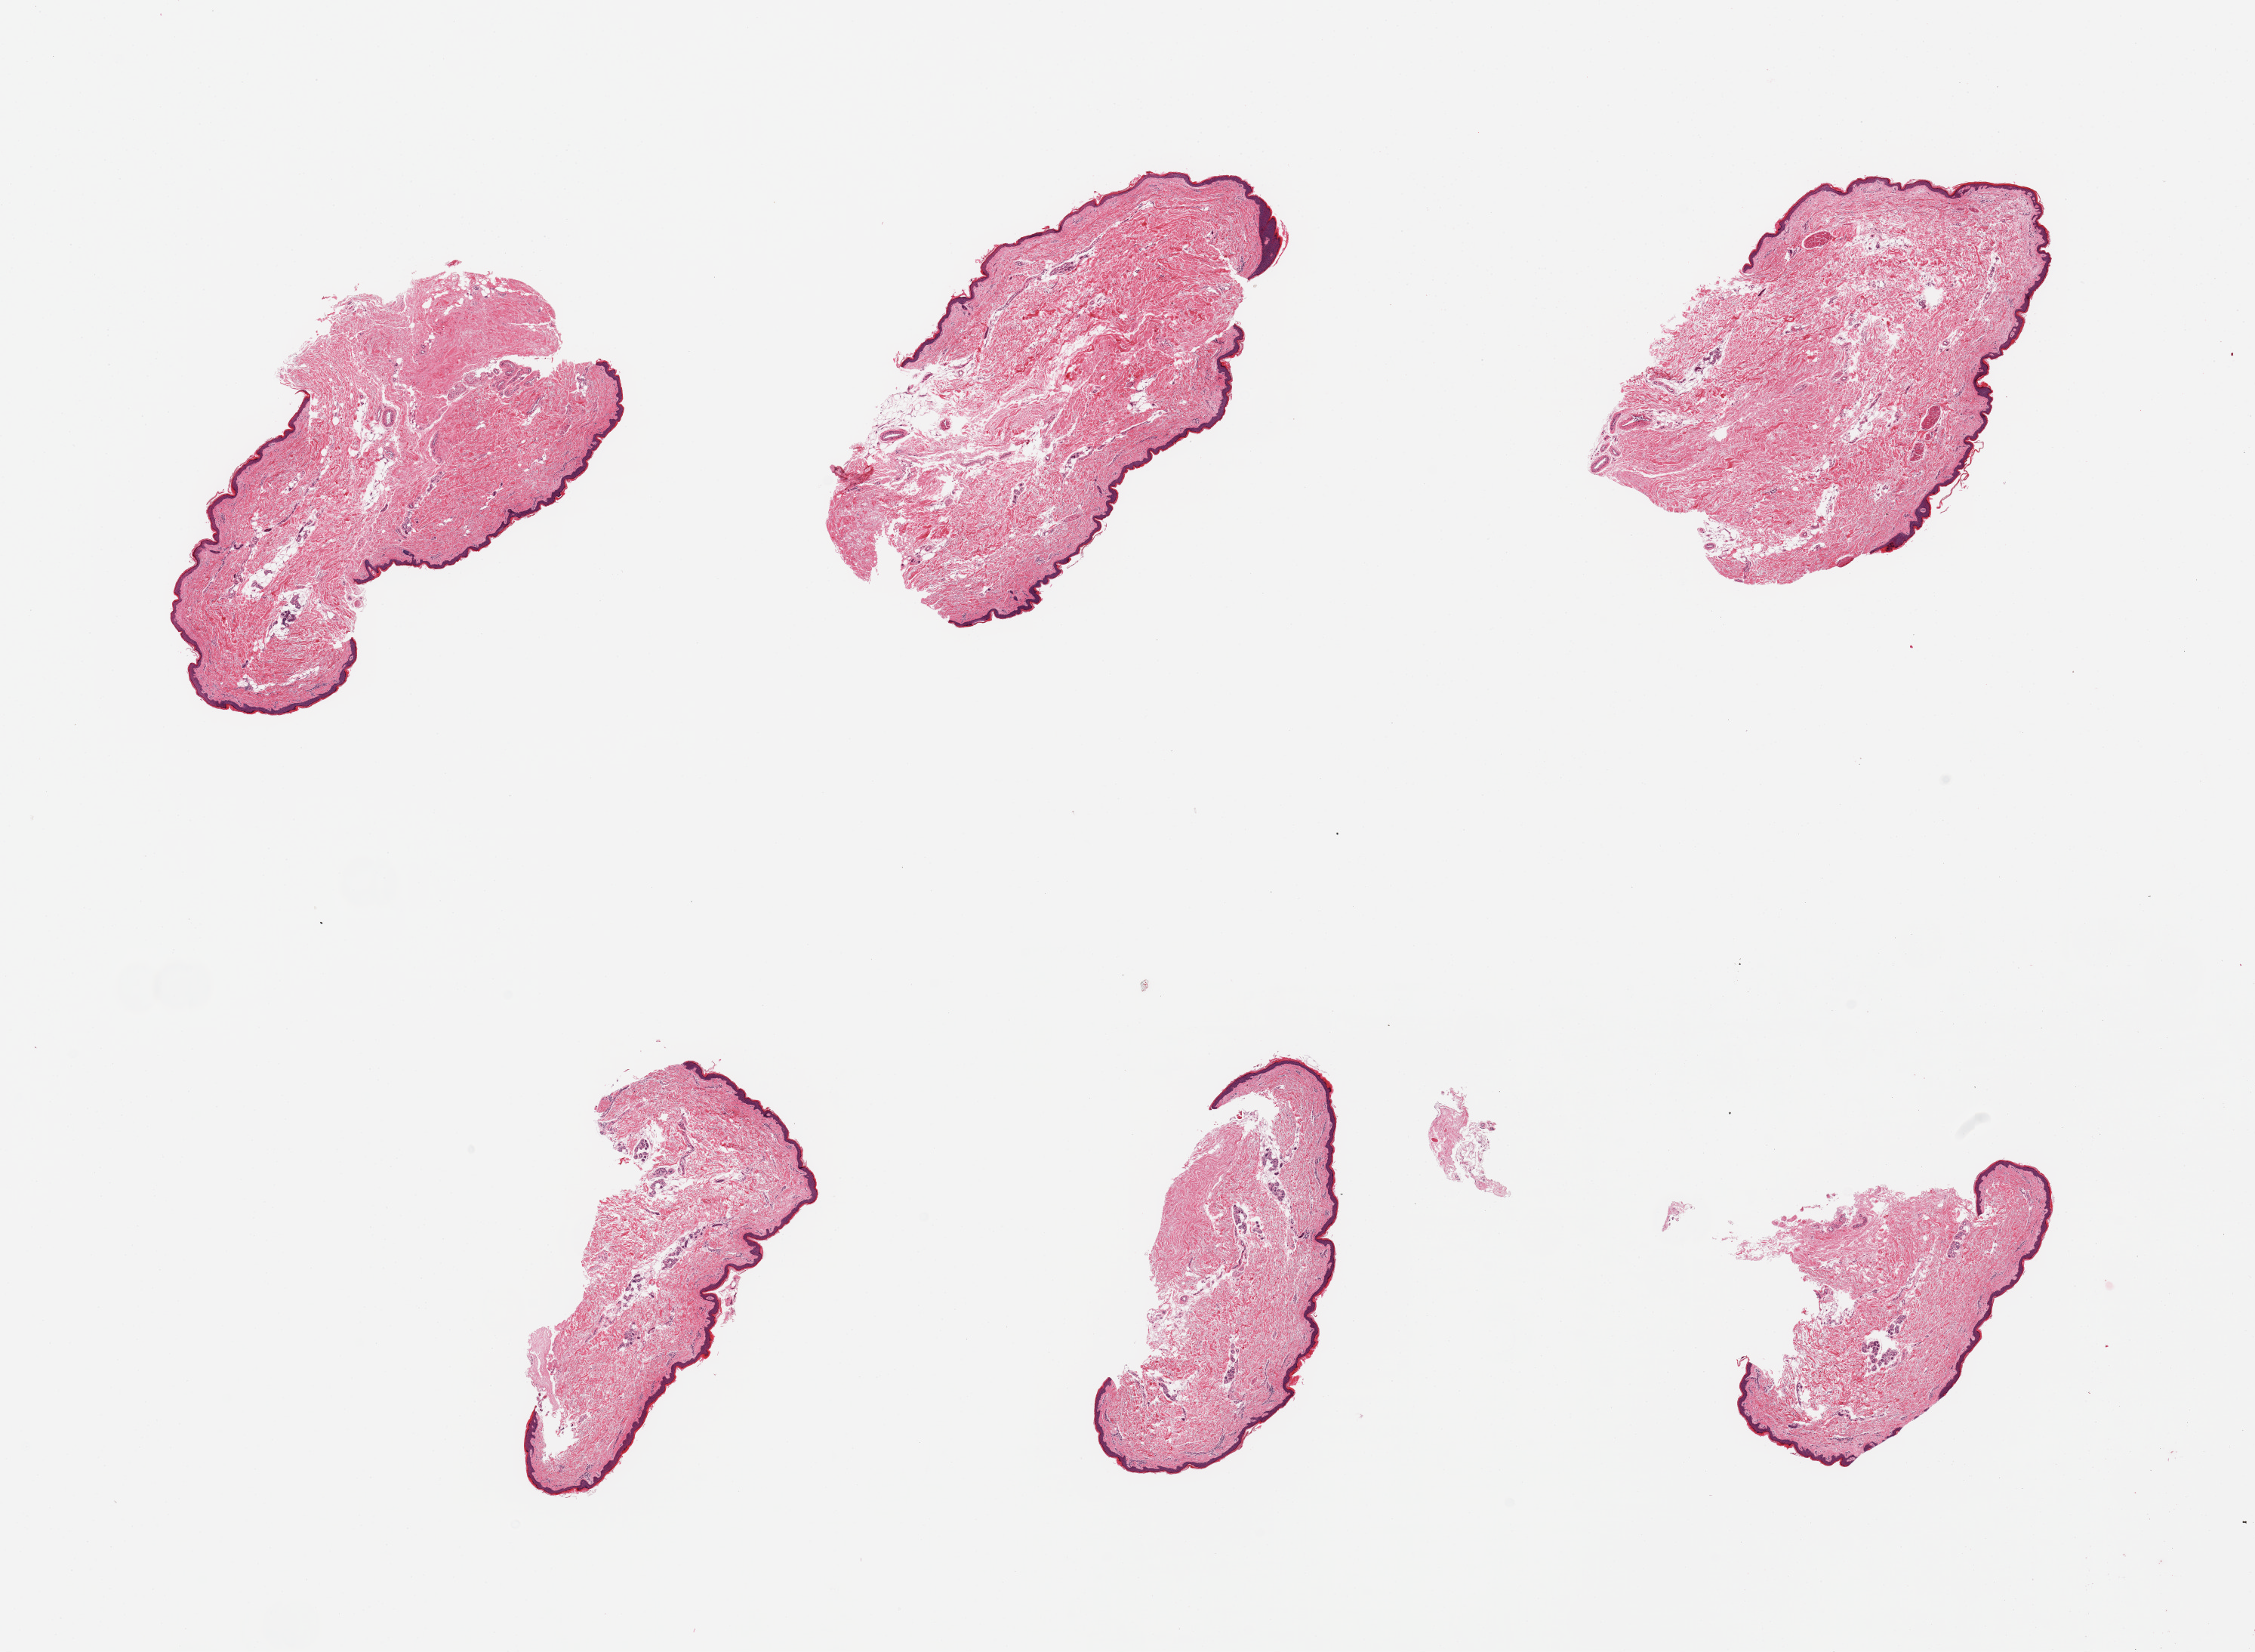
Whole-slide image, H&E stain, brightfield, whole scanned area (about 23.6 x 17.3 mm) shown as a low-resolution overview; PAXgene-fixed, paraffin-embedded tissue; target tissue: skin of lower leg; donor tissue sample. Donor sex: female.
* pathologist's review note for this sample: 6 pieces; well trimmed; <5% intradermal fat